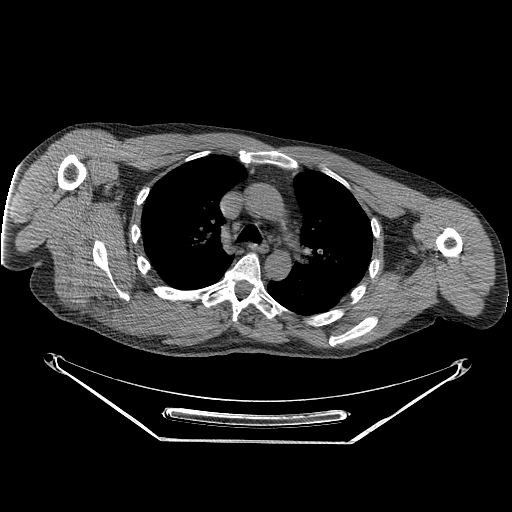
CT of an extremity soft-tissue mass (from a PET/CT study), one axial slice. Position 184 of 267 along the scan axis. Reconstruction kernel STANDARD. Soft-tissue window (W 400 / L 40 HU). 512 × 512 image matrix, field of view 500 × 500 mm. Male patient. From the clinical record (not read from this slice): histological type: pleiomorphic spindle cell undifferentiated; grade: high; site of the primary tumour: right parascapusular.
Outlined on this slice (expert contour drawn on MRI and transferred to this co-registered scan by the dataset authors):
- gross tumour volume including surrounding oedema: box from (x=82, y=281) to (x=216, y=337) px
- gross tumour volume (mass): (x=94, y=283)–(x=179, y=332)